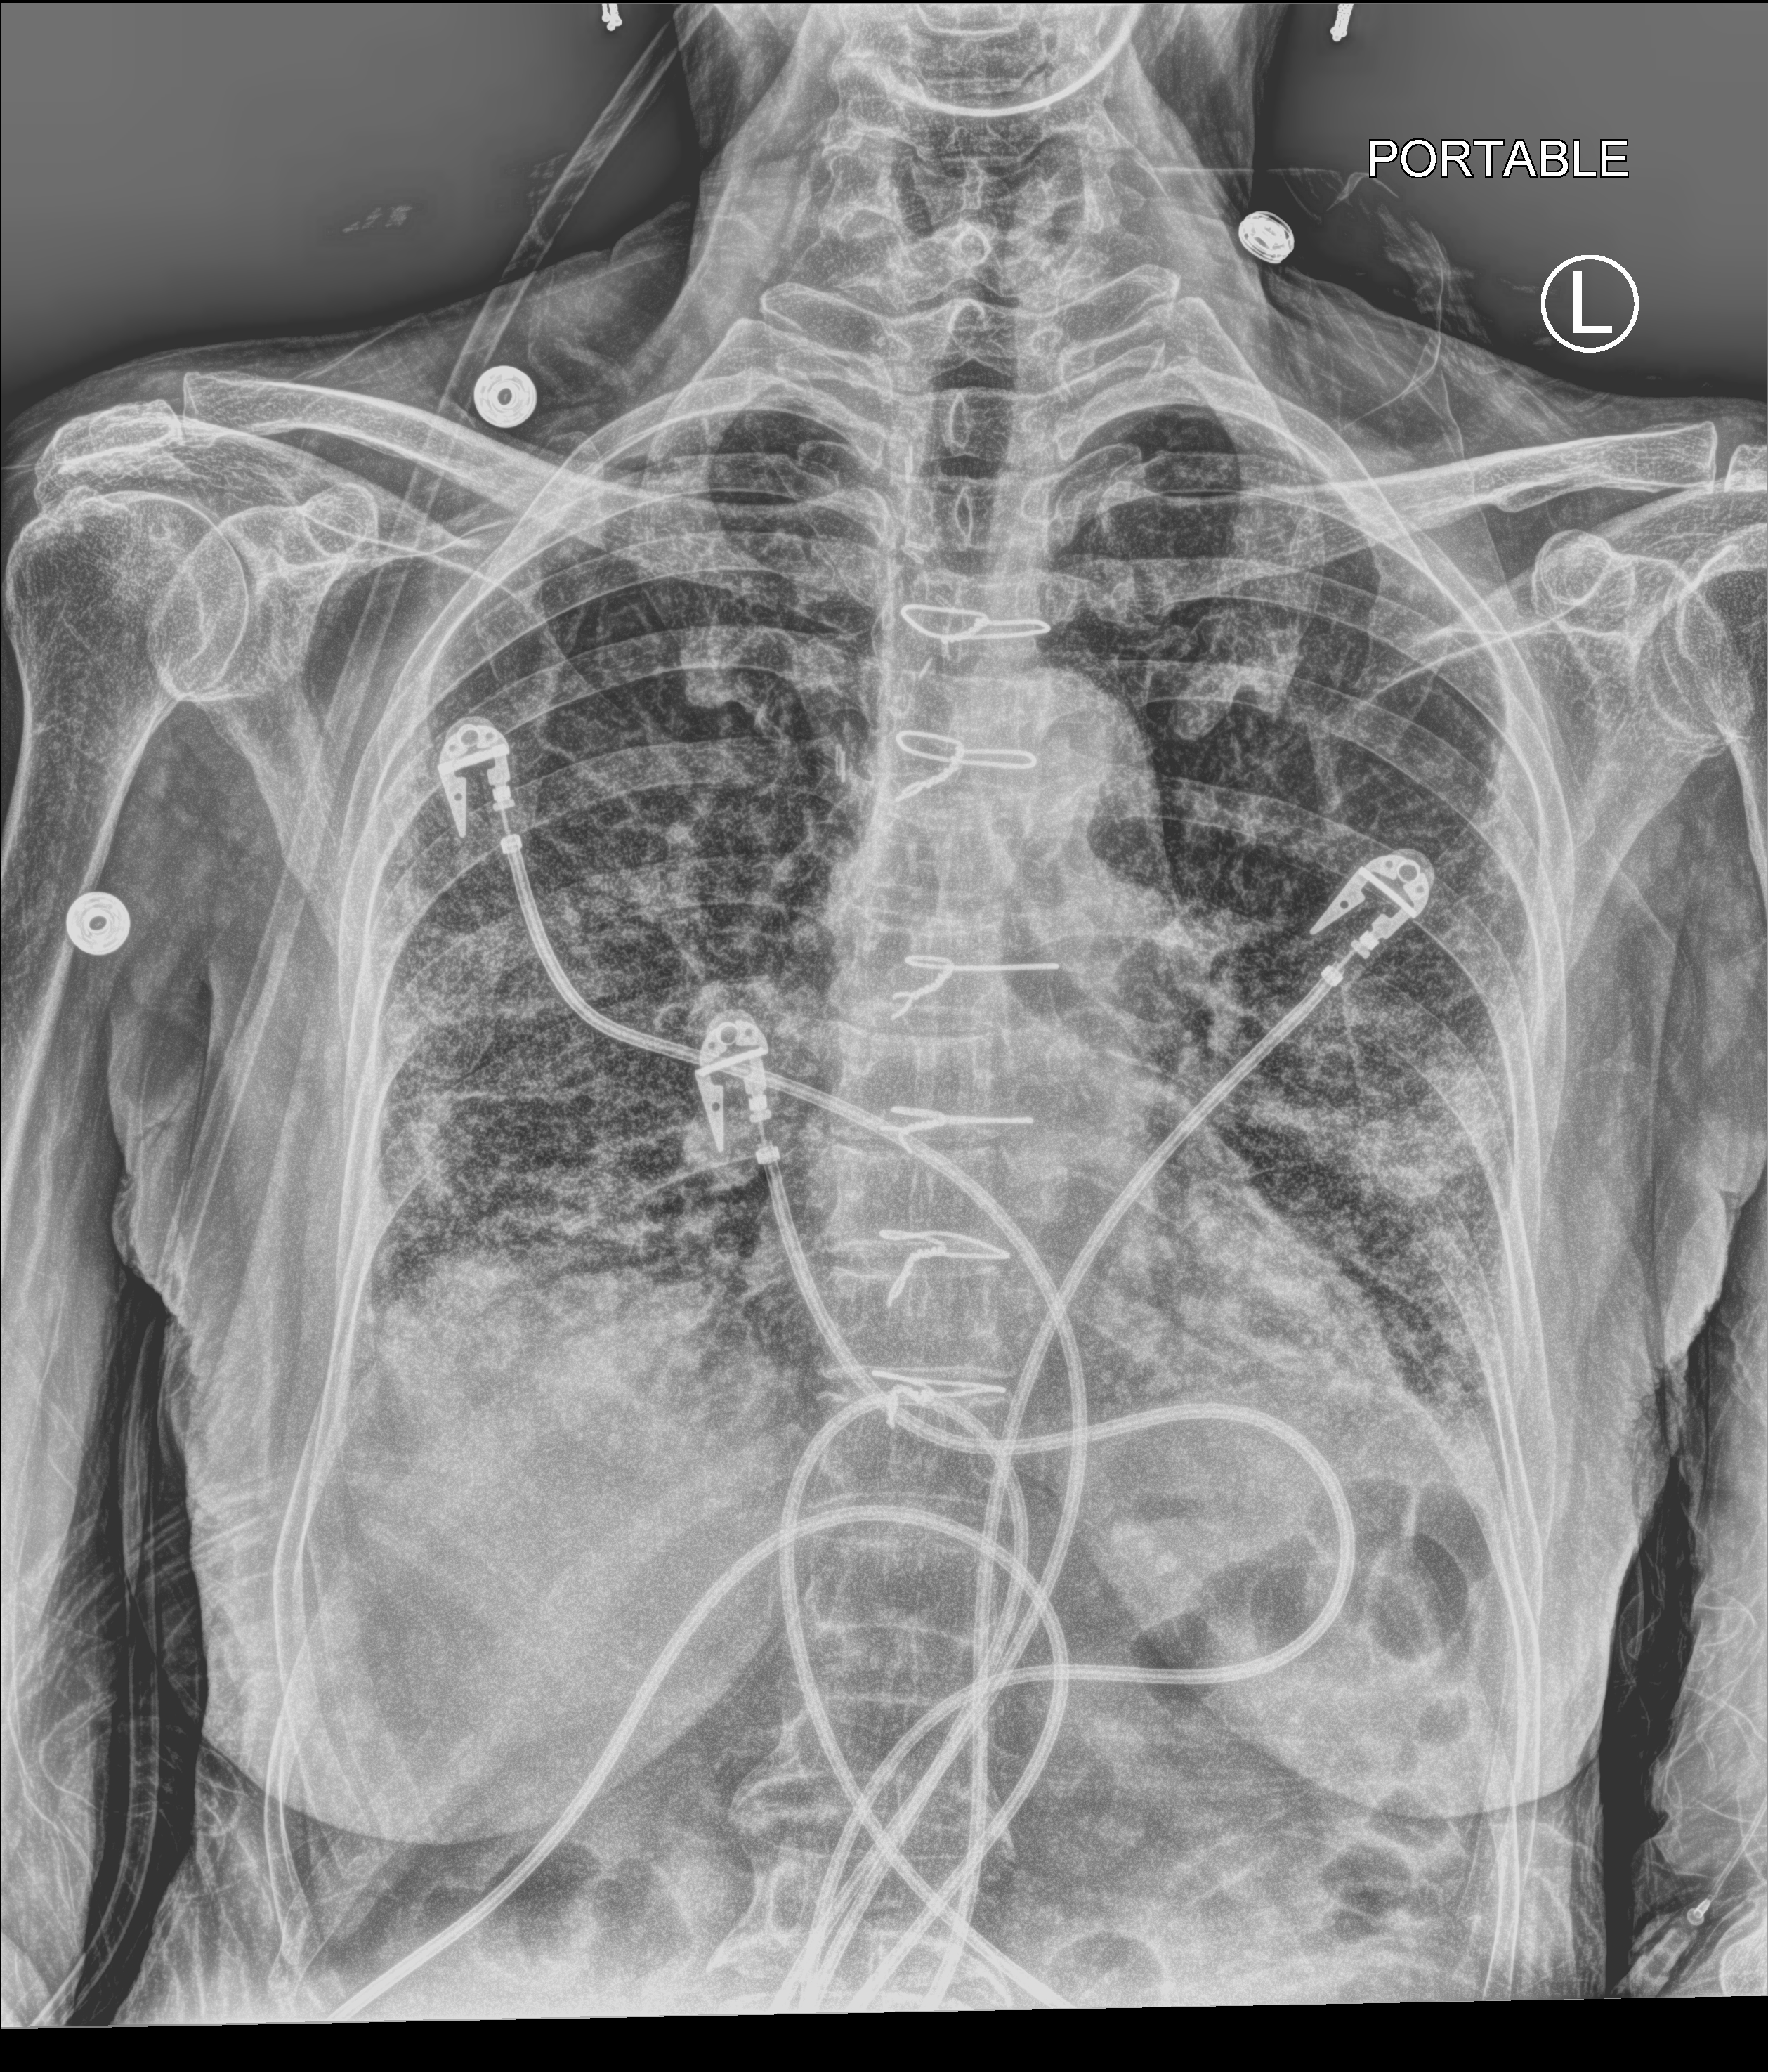
Chest X-ray (portable); anteroposterior (AP) projection. Female patient hospitalised with COVID-19, age 75–90 years.
Admission-level facts for this patient (not findings on this image; timing relative to this image not recorded): hypertension (admission record): yes; chronic kidney disease (admission record): no.